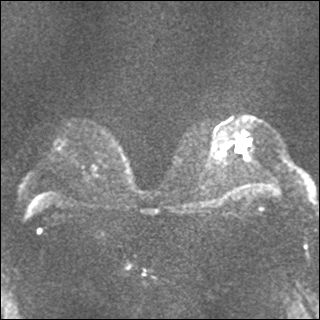
Breast MRI, one axial slice; slice 21 of 35 in the series (ordered by position); diffusion-weighted series; image 2 of 4 stored at this slice position (different b-values; order by instance number); 1.5 T; 4 mm slice thickness; 320 × 320 image matrix, field of view 320 × 320 mm. Female patient.
Structures marked on this image (expert manual segmentation):
- tumour on diffusion-weighted imaging: bounding box [x1, y1, x2, y2] px = [238, 139, 244, 151]